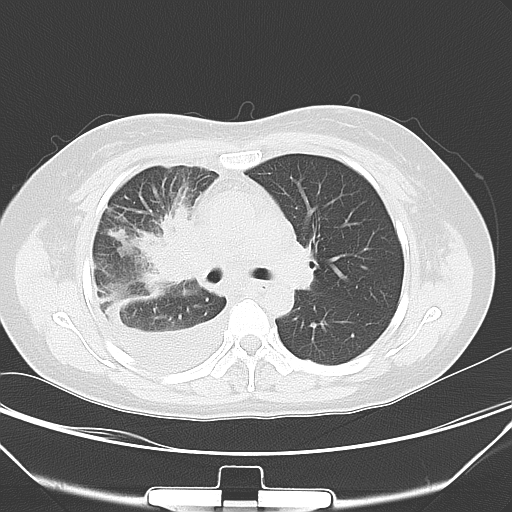
Chest CT, one axial slice. Position 33 of 52 along the scan axis. 120 kVp. Lung window (W 1500 / L -600 HU). 512 × 512 image matrix. Patient: female, 36 years. From the clinical record (not read from this slice): clinical TNM (as recorded): T1b N2 M0; histopathological grade: G3.
Structures marked on this image (rectangle marked by the reading radiologist):
- lung tumour (recorded histology: adenocarcinoma): bounding box <122,201,201,292> (left, top, right, bottom; pixels)